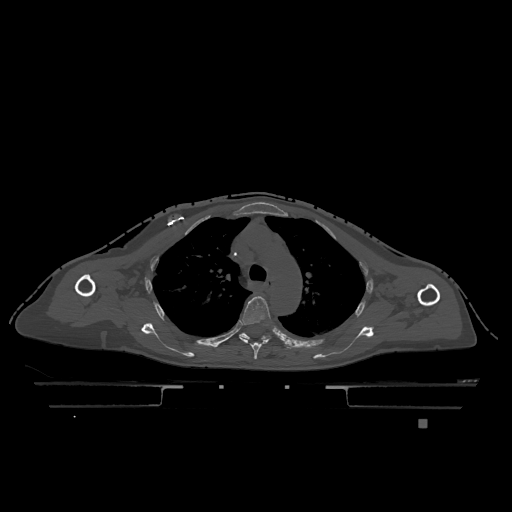
CT including the spine, one axial slice; position 867 of 1317 along the scan axis; bone window (W 1800 / L 400 HU); 512 × 512 image matrix, field of view 500 × 500 mm. Female patient, age 74 years. Case-level facts recorded for this patient, not image findings: primary cancer: lung.
Structures marked on this image (semi-automatic segmentation, software-assisted and operator-edited):
- T4 vertebra: bounding box <239,296,271,360> (left, top, right, bottom; pixels)
- T5 vertebra: <239,333,269,339>